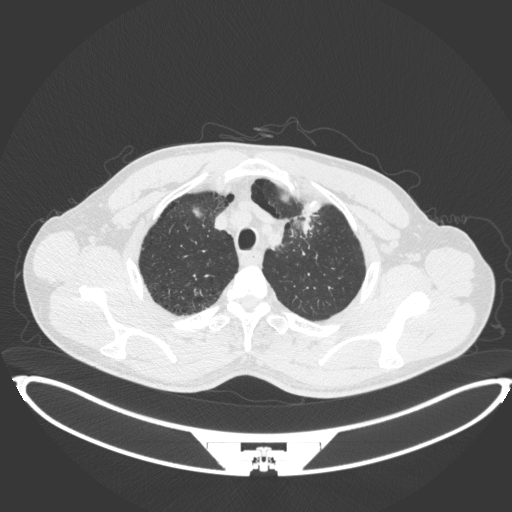
Chest CT, one axial slice; slice 369 of 407 in the series (ordered by position); 120 kVp; lung window (W 1500 / L -600 HU); 1 mm slice thickness; 512 × 512 image matrix. Male patient, age 60 years. Case-level facts recorded for this patient, not image findings: clinical TNM (as recorded): T2a N0 M0; histopathological grade: G1-G2.
Annotated regions visible in this slice (rectangle marked by the reading radiologist):
- lung tumour (recorded histology: squamous cell carcinoma): bounding box (x1, y1, x2, y2) in pixels: (287, 214, 317, 241)